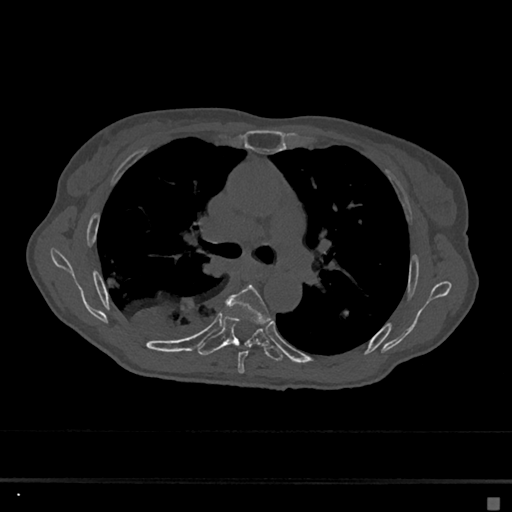
CT including the spine, one axial slice; position 439 of 797 along the scan axis; 120 kVp; bone window (W 1800 / L 400 HU); 512 × 512 image matrix, field of view 360 × 360 mm. Patient: female, 68 years. Case-level facts recorded for this patient, not image findings: primary cancer: renal.
Annotated regions visible in this slice (semi-automatically segmented with operator editing):
- T5 vertebra: box from (x=226, y=285) to (x=271, y=374) px
- T6 vertebra: (x=197, y=314)–(x=283, y=362)